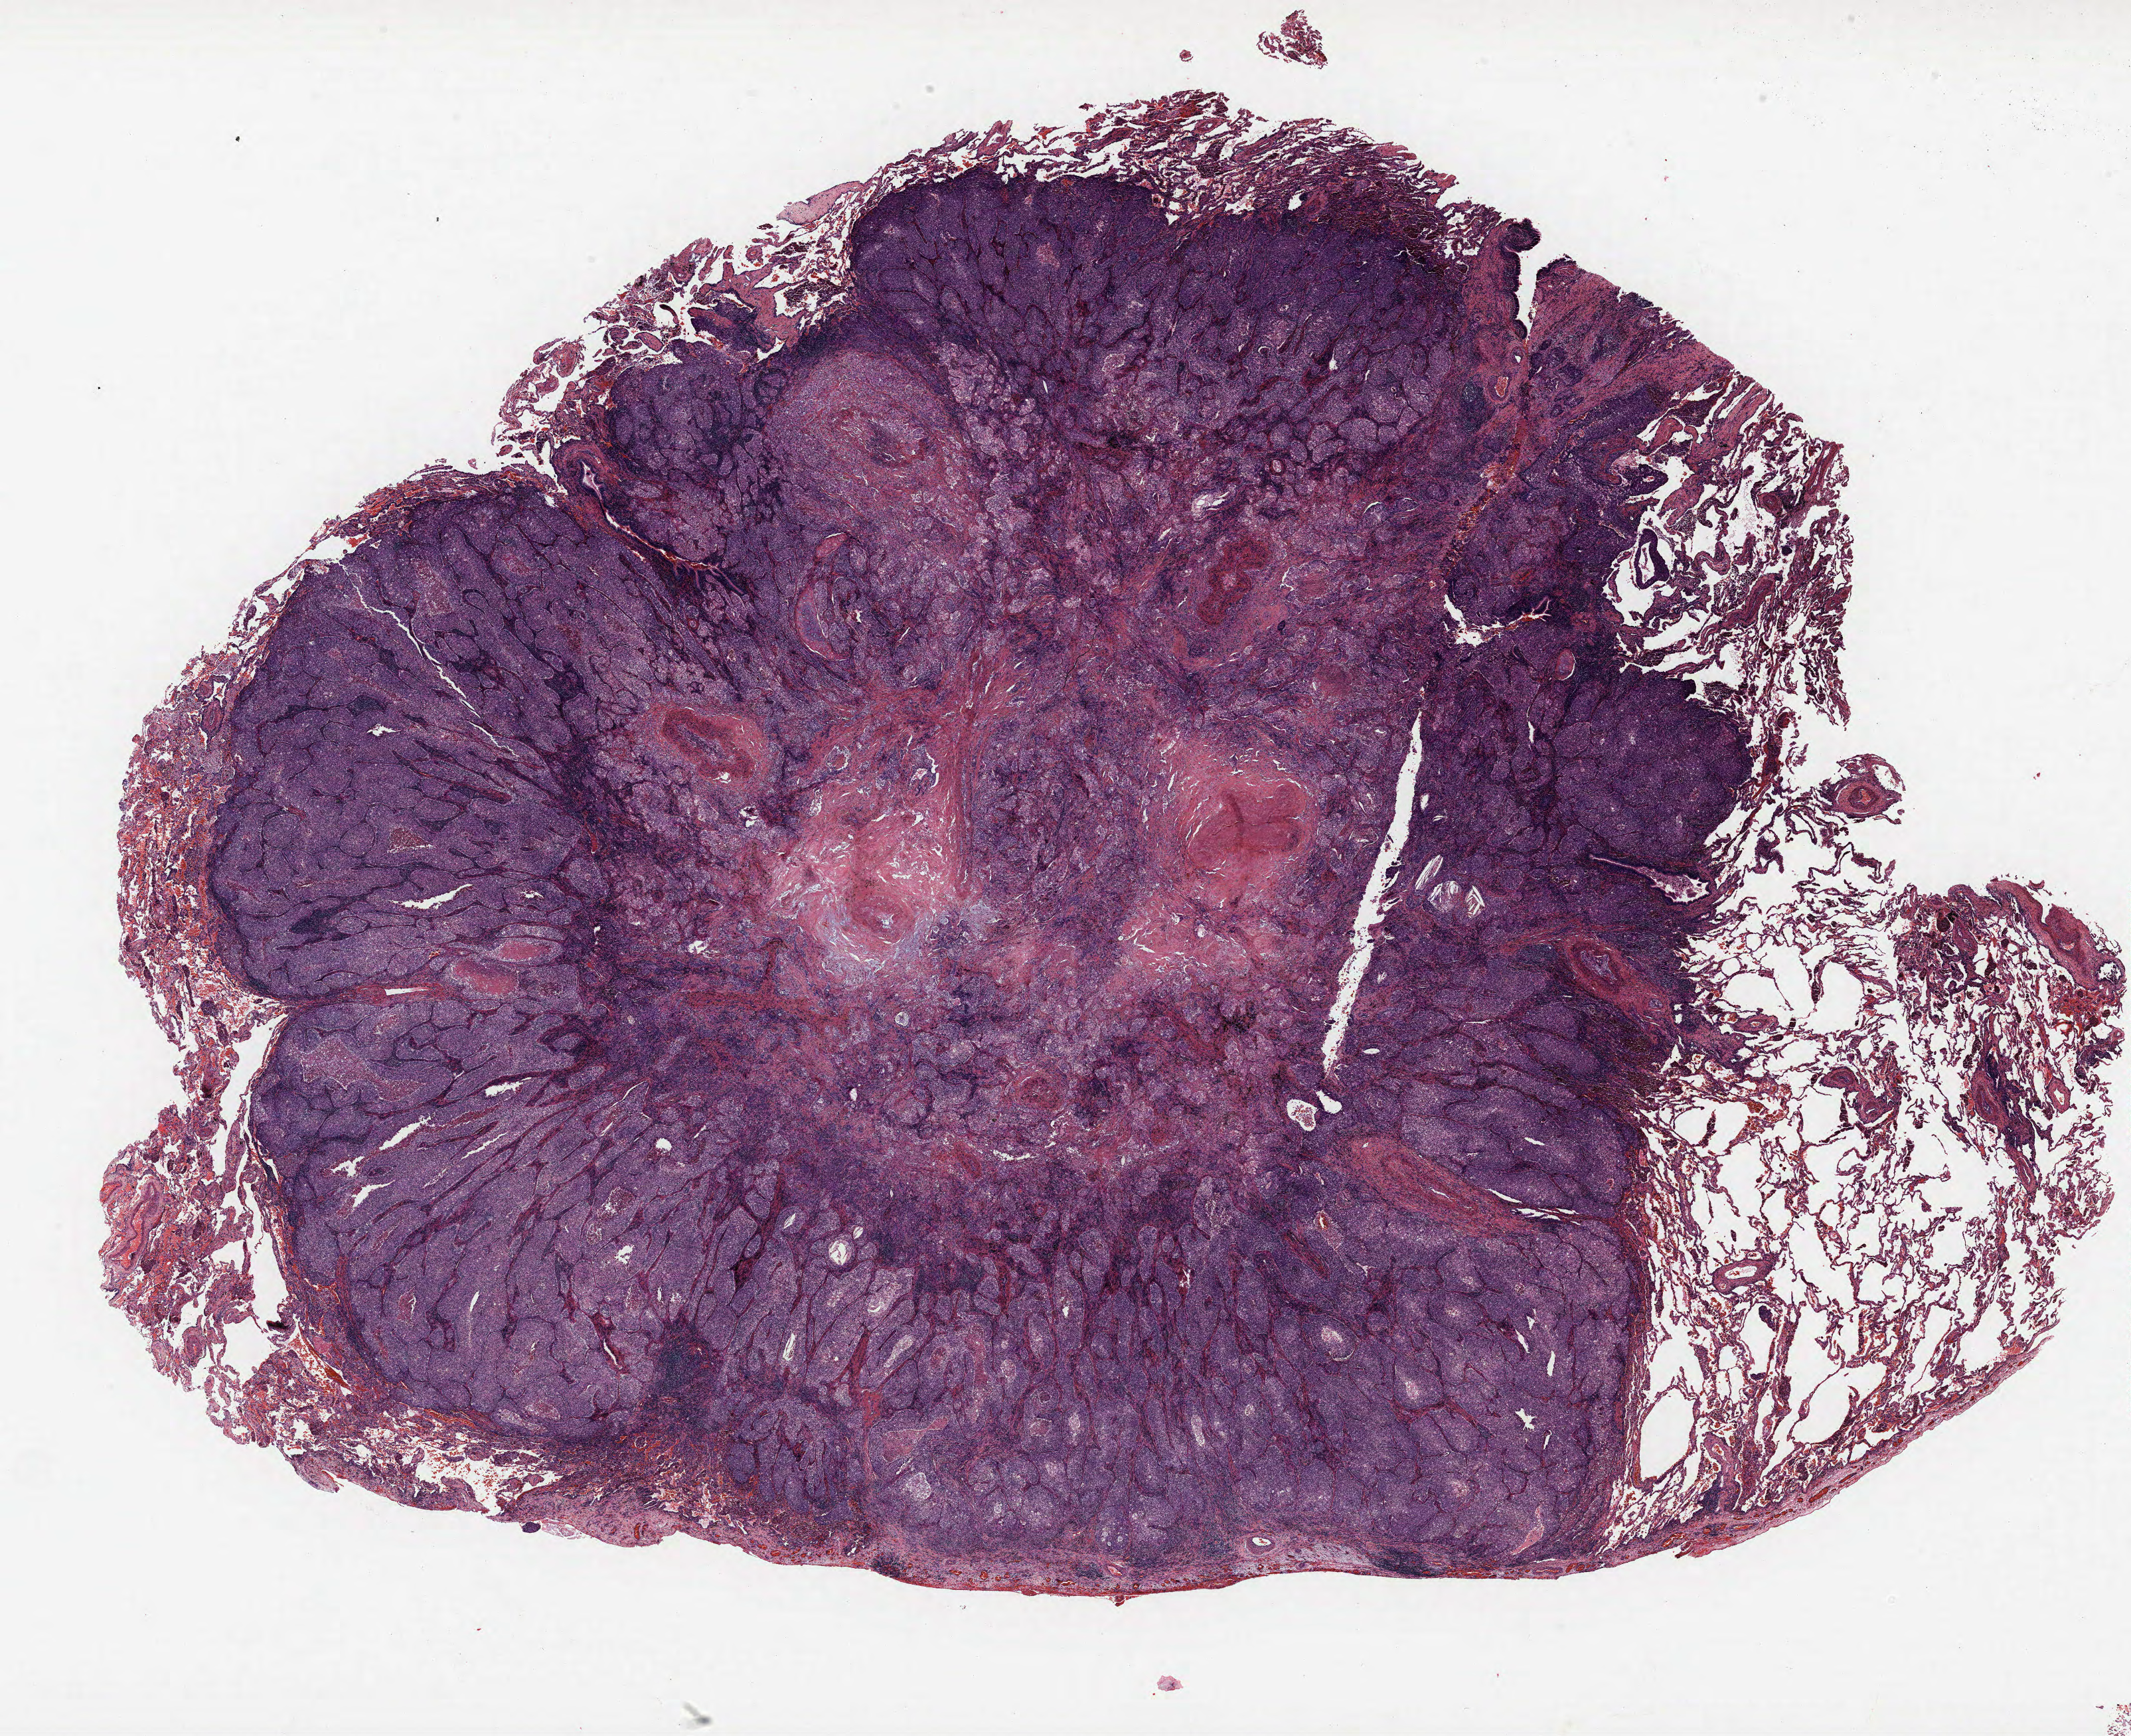
Whole-slide histology image, Hematoxylin and eosin (H&E) stained, shown as a low-resolution overview of the whole scanned area (about 25.7 x 20.9 mm), formalin-fixed paraffin-embedded (FFPE) section, lung tissue. Female, age 56 at enrolment. Current smoker at enrolment. Grade: poorly differentiated (G3).
Primary tumour location (clinical record): right upper lobe. Stage (AJCC 6th edition): IIA. Participant's lung-cancer diagnosis: Adenocarcinoma, NOS. Tumour size (pathology): 20 mm.